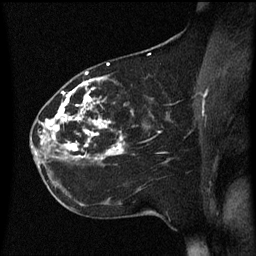
Breast MRI (dynamic contrast-enhanced), one sagittal slice; slice 28 of 60 in the series (ordered by position); dynamic contrast-enhanced series, image 2 of 3 at this slice position (ordered by acquisition); 1.5 T; TE 4.2 ms, TR 8.4 ms; 2.2 mm slice thickness; 256 × 256 image matrix, field of view 200 × 200 mm. Female patient, age 35 years. From the clinical record (not read from this slice): setting: breast cancer imaged before/during neoadjuvant chemotherapy; receptor status: HER2-positive.
Annotated regions visible in this slice (semi-automatically segmented with operator editing):
- analysis volume of interest (the breast-tissue region the enhancement analysis was run in; not a lesion): bounding box <32,78,173,163> (left, top, right, bottom; pixels)
- tumour enhancement mask (voxels above the 70 % enhancement threshold inside the analysis volume of interest): <32,78,125,155>